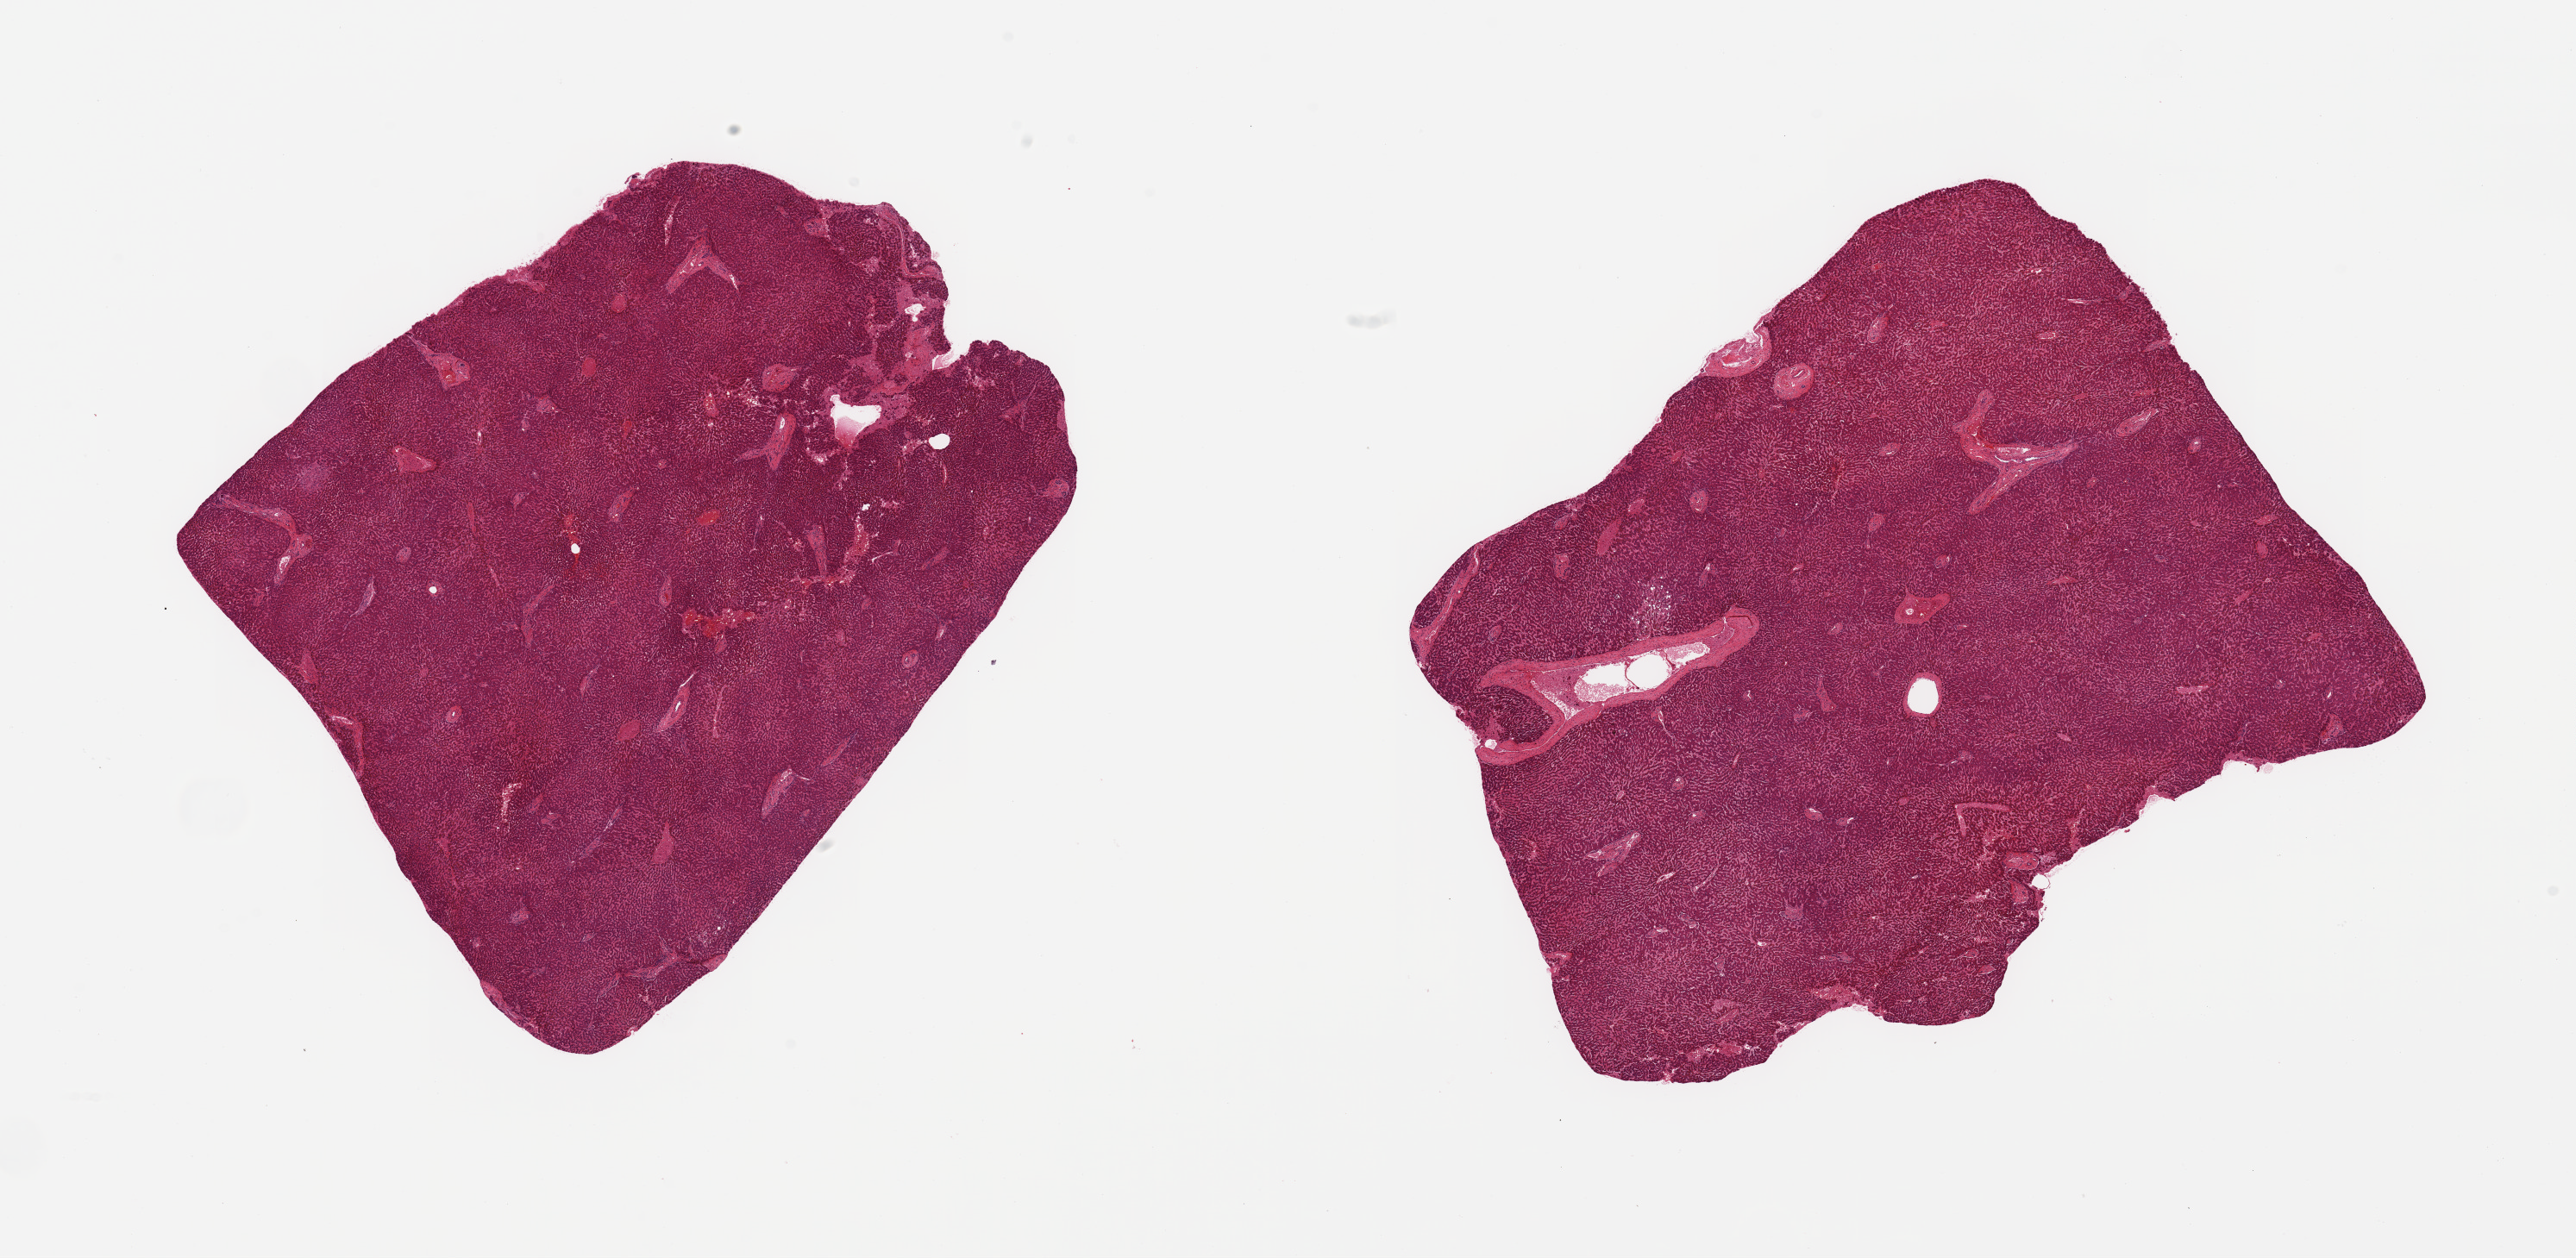
Whole-slide image, haematoxylin and eosin stain, a low-resolution overview of the entire scanned area, about 23.6 x 11.5 mm (from a 20x scan). PAXgene-fixed paraffin-embedded (PFPE) section. Target tissue: liver. Donor tissue sample. Donor sex: male.
* pathologist's review note for this sample: 2 pieces, mild passive congestion